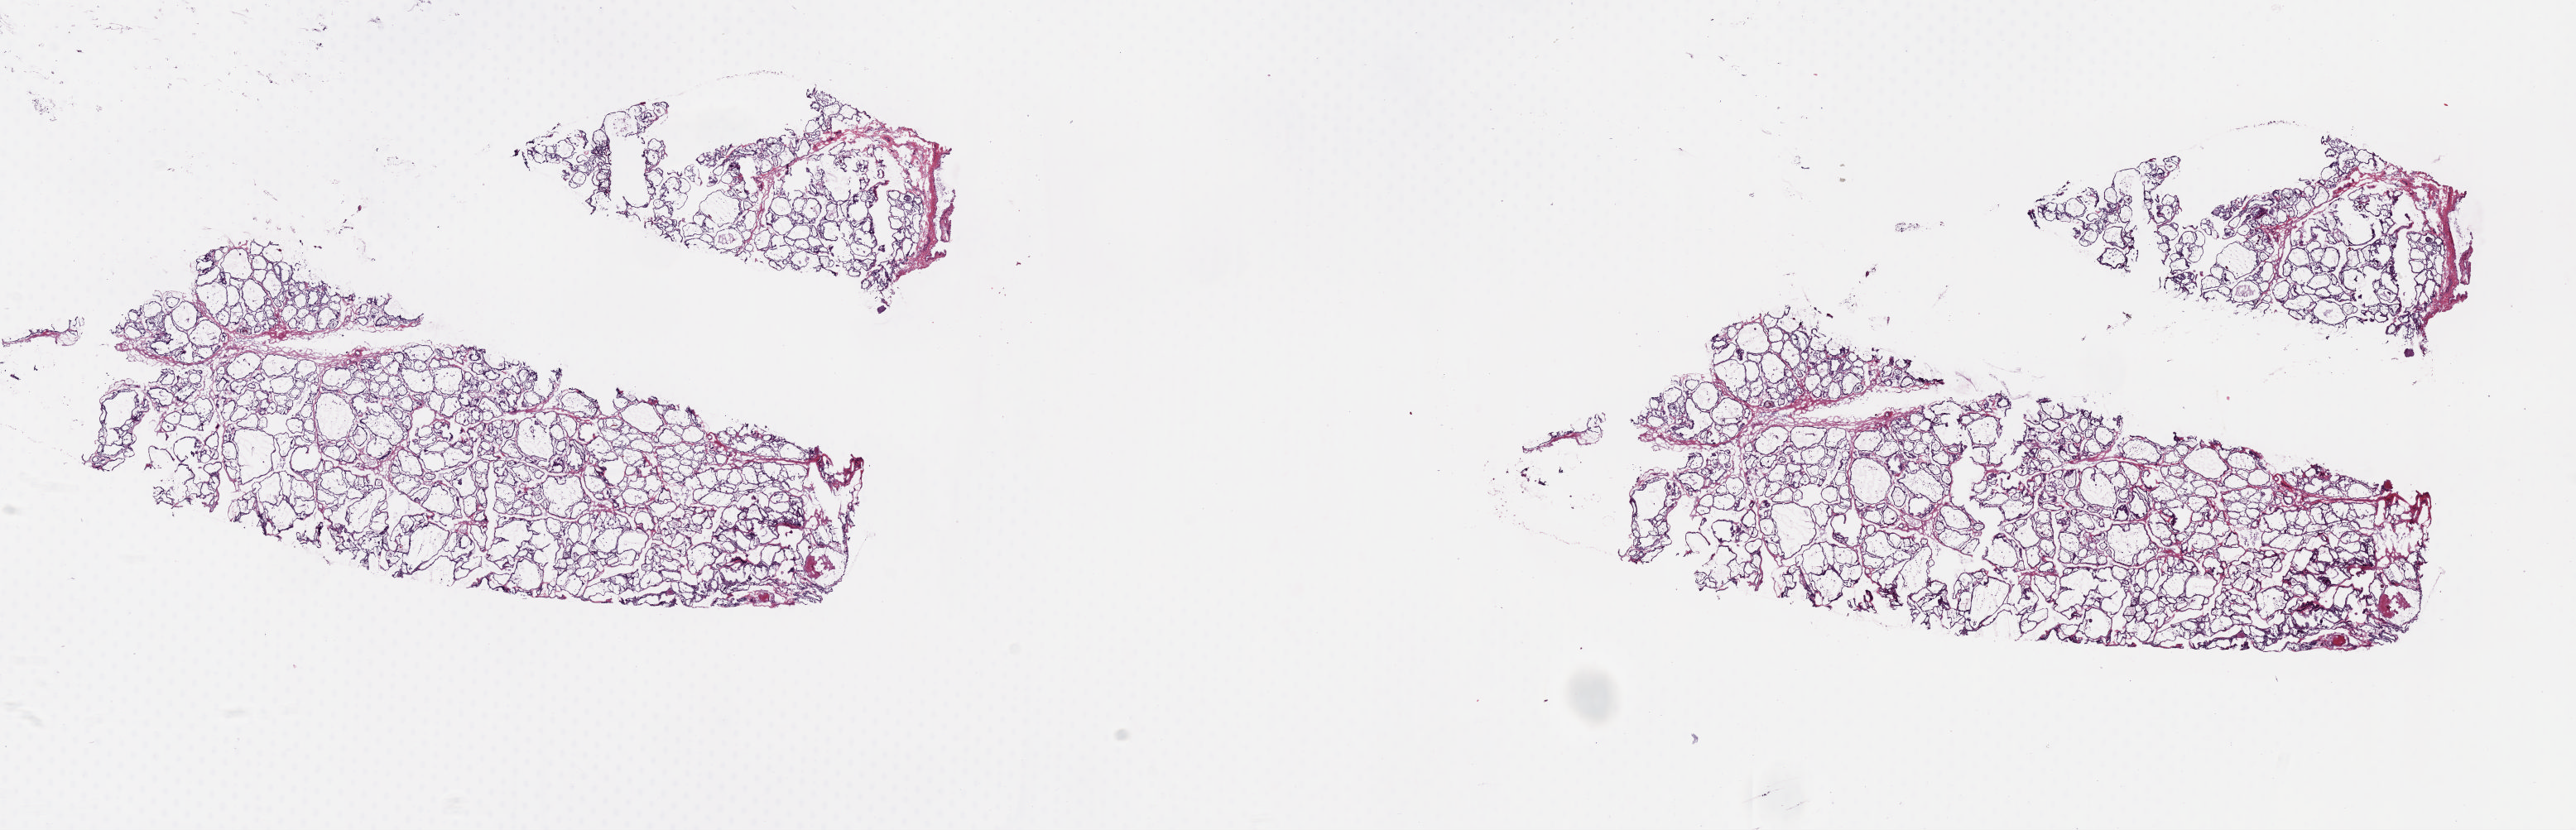
Digitized Hematoxylin and eosin (H&E) stained tissue section (whole slide) — shown as a low-resolution overview of the whole scanned area (about 24.5 x 7.9 mm, acquisition: 20x scan). Frozen section. Solid tissue normal (non-tumour tissue) sample from the thyroid. Female patient; age at initial diagnosis 45 years. Slide review estimates, as recorded: tumour cells 0%, tumour nuclei 0%, normal cells 100%, stromal cells 0%, necrosis 0%. Inflammatory infiltration, as recorded: lymphocyte infiltration 0%, monocyte infiltration 0%, neutrophil infiltration 0%.
This section: solid tissue normal sample (biorepository sample class). Patient diagnosis: Papillary adenocarcinoma, NOS (thyroid gland).